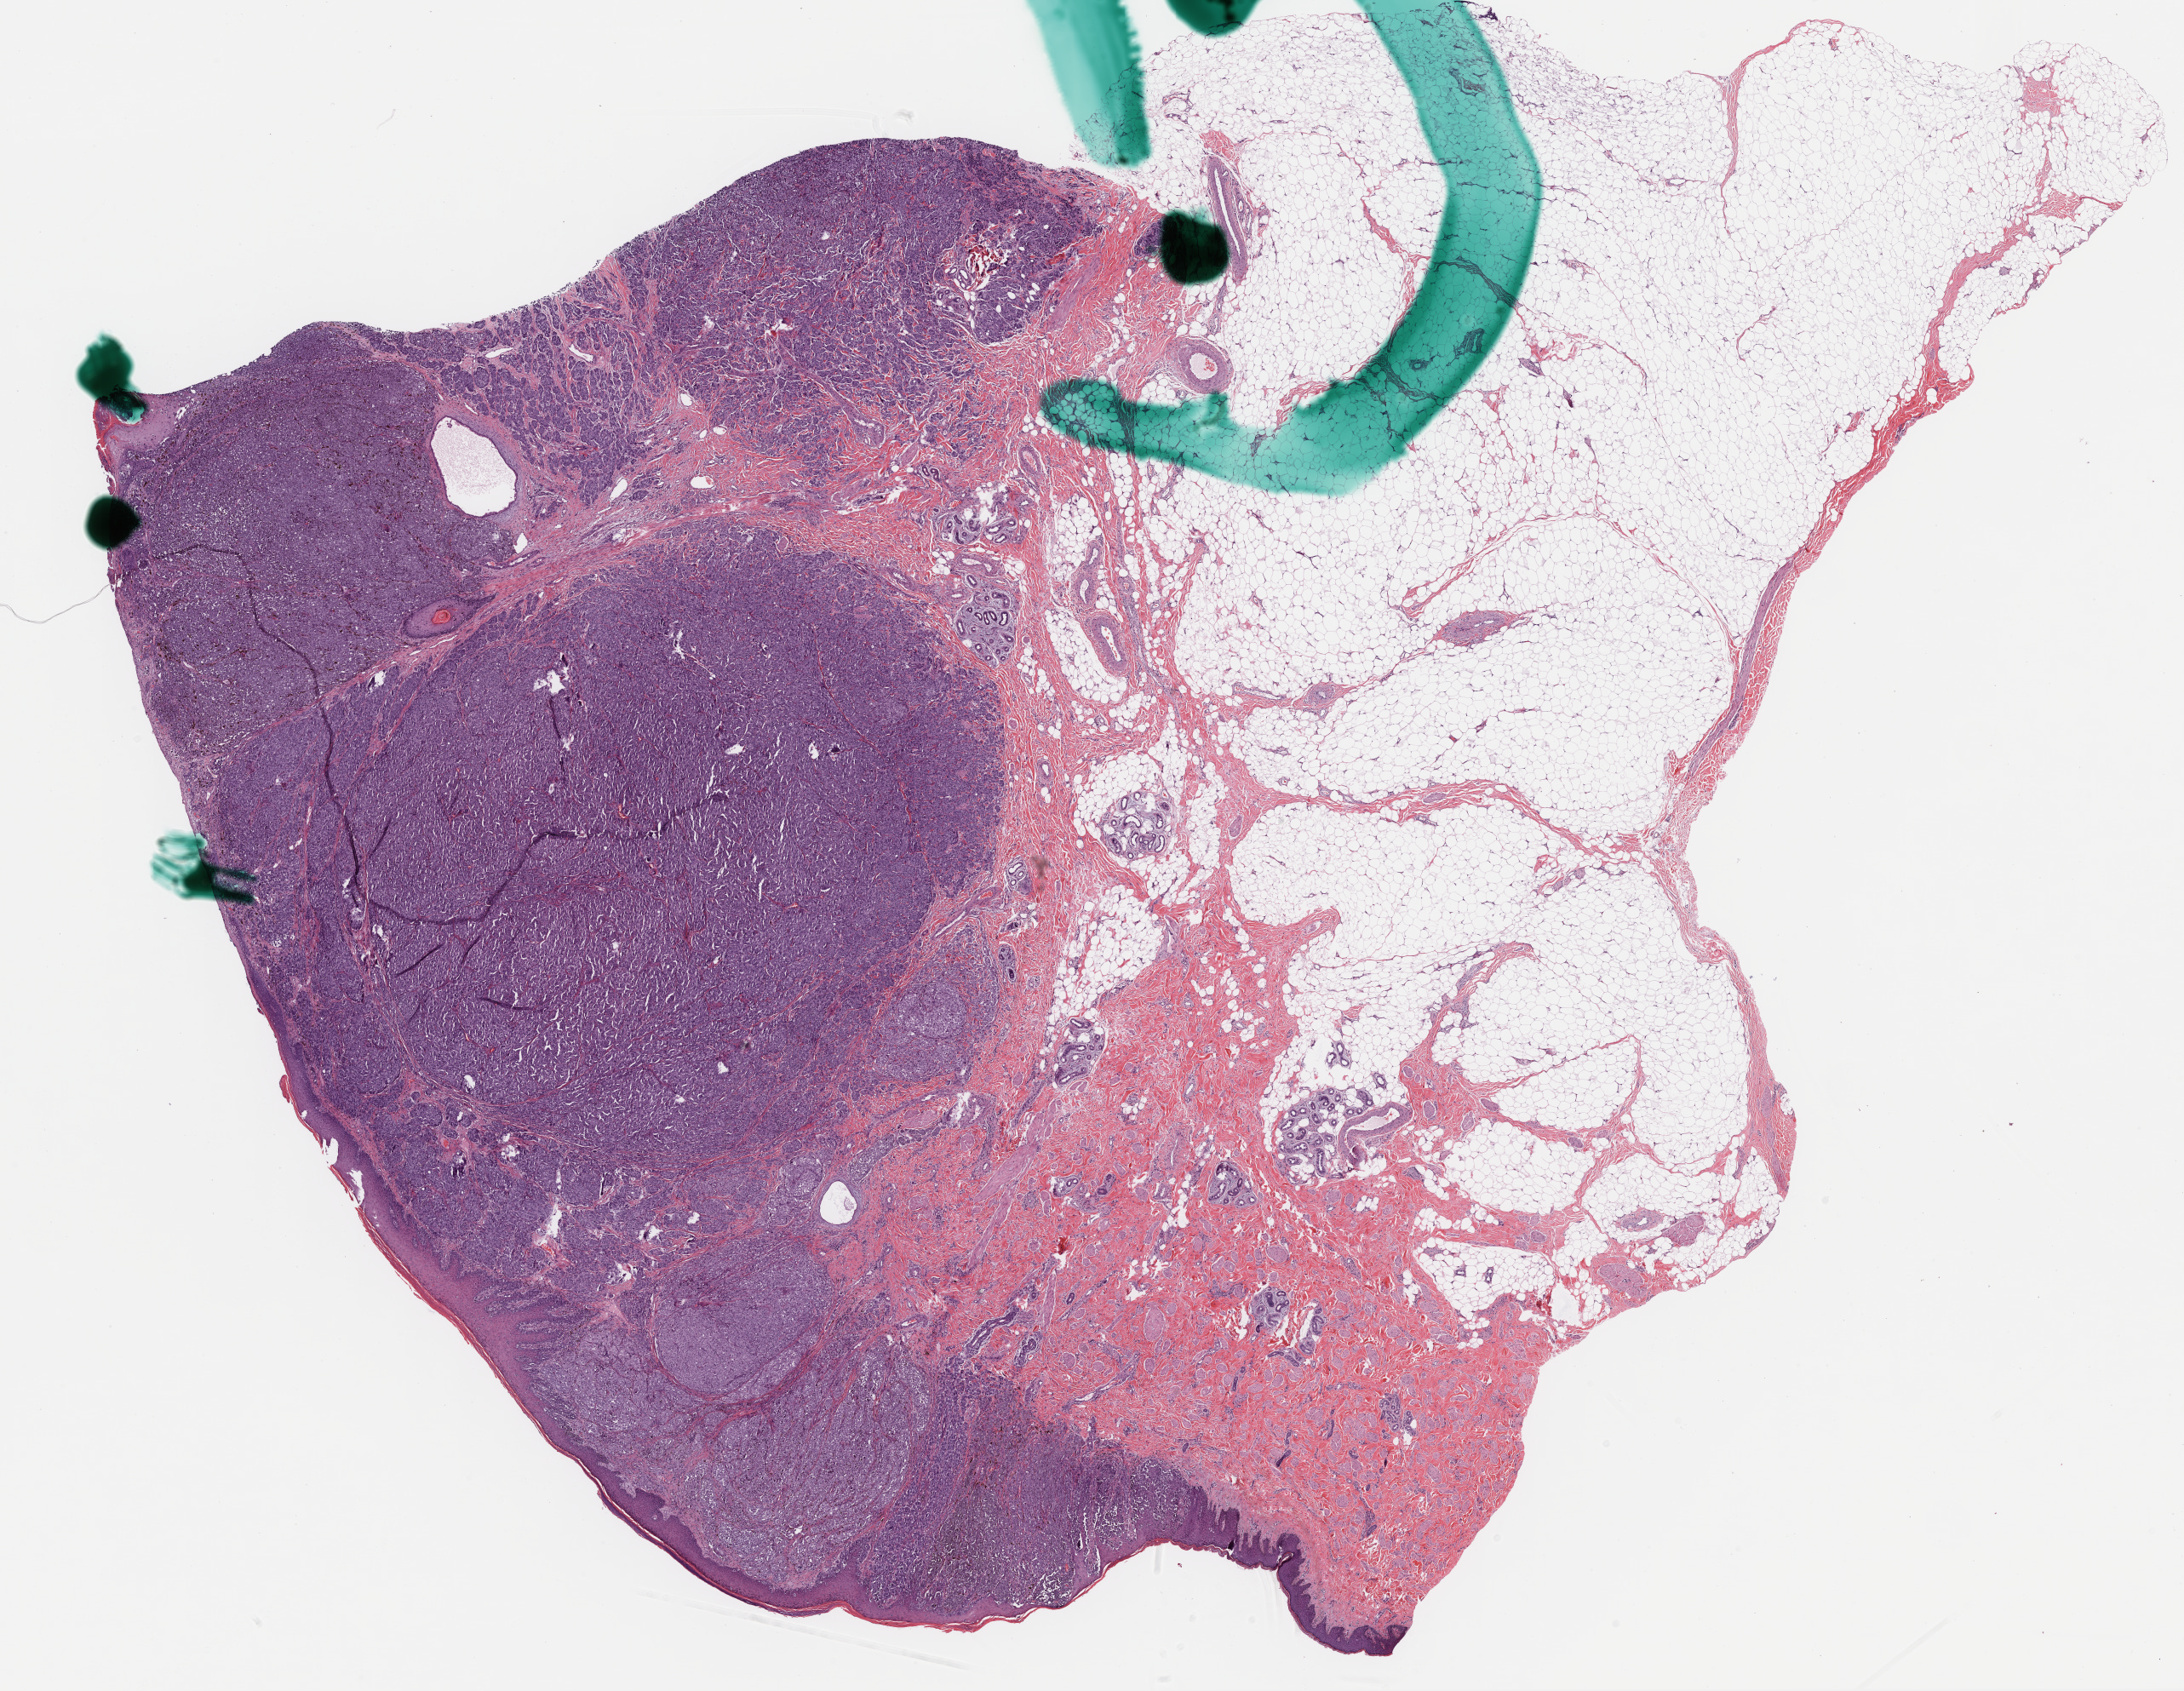
Digitized H&E tissue section (whole slide) — whole scanned area (about 20.7 x 16.0 mm, from a 20x scan) shown as a low-resolution overview, formalin-fixed paraffin-embedded (FFPE) diagnostic section, metastatic tumour sample, sampled site not recorded. Patient: male, age at initial diagnosis 43 years.
This section: metastatic tumour tissue. Patient diagnosis: Malignant melanoma, NOS.